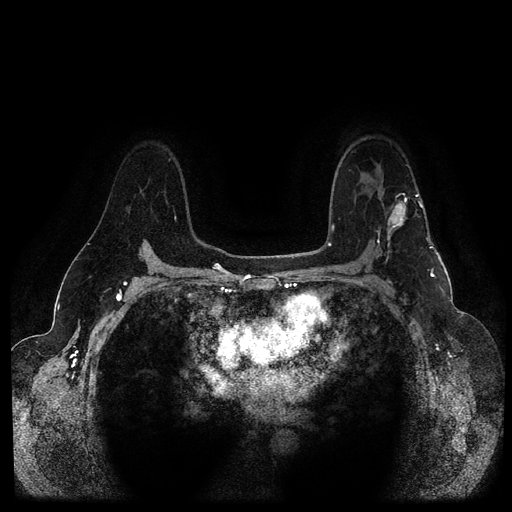
Breast MRI (dynamic contrast-enhanced, multi-phase), one axial slice. Position 73 of 116 along the scan axis. Dynamic contrast-enhanced series, time point 2 of 5 at this slice position (early post-contrast). 1.5 T. TE 2.6 ms, TR 5.3 ms. 2 mm slice thickness. 512 × 512 image matrix, field of view 350 × 350 mm. Female patient, age 54 years.
Outlined on this slice (semi-automatically segmented with operator editing):
- breast lesion (labelled 'tumour' in the annotation; benign lesions carry a separate 'benign' label): box from (x=385, y=193) to (x=410, y=241) px